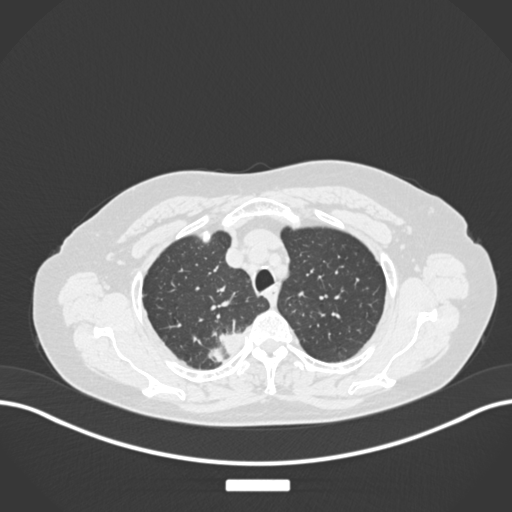
Chest CT, one axial slice. Position 211 of 237 along the scan axis. Lung window (W 1500 / L -600 HU). 512 × 512 image matrix, field of view 400 × 400 mm. Female patient, age 62 years. Case-level facts recorded for this patient, not image findings: clinical TNM (as recorded): T1c N1 M0.
Structures marked on this image (rectangle marked by the reading radiologist):
- lung tumour (recorded histology: squamous cell carcinoma): bounding box <201,321,251,368> (left, top, right, bottom; pixels)